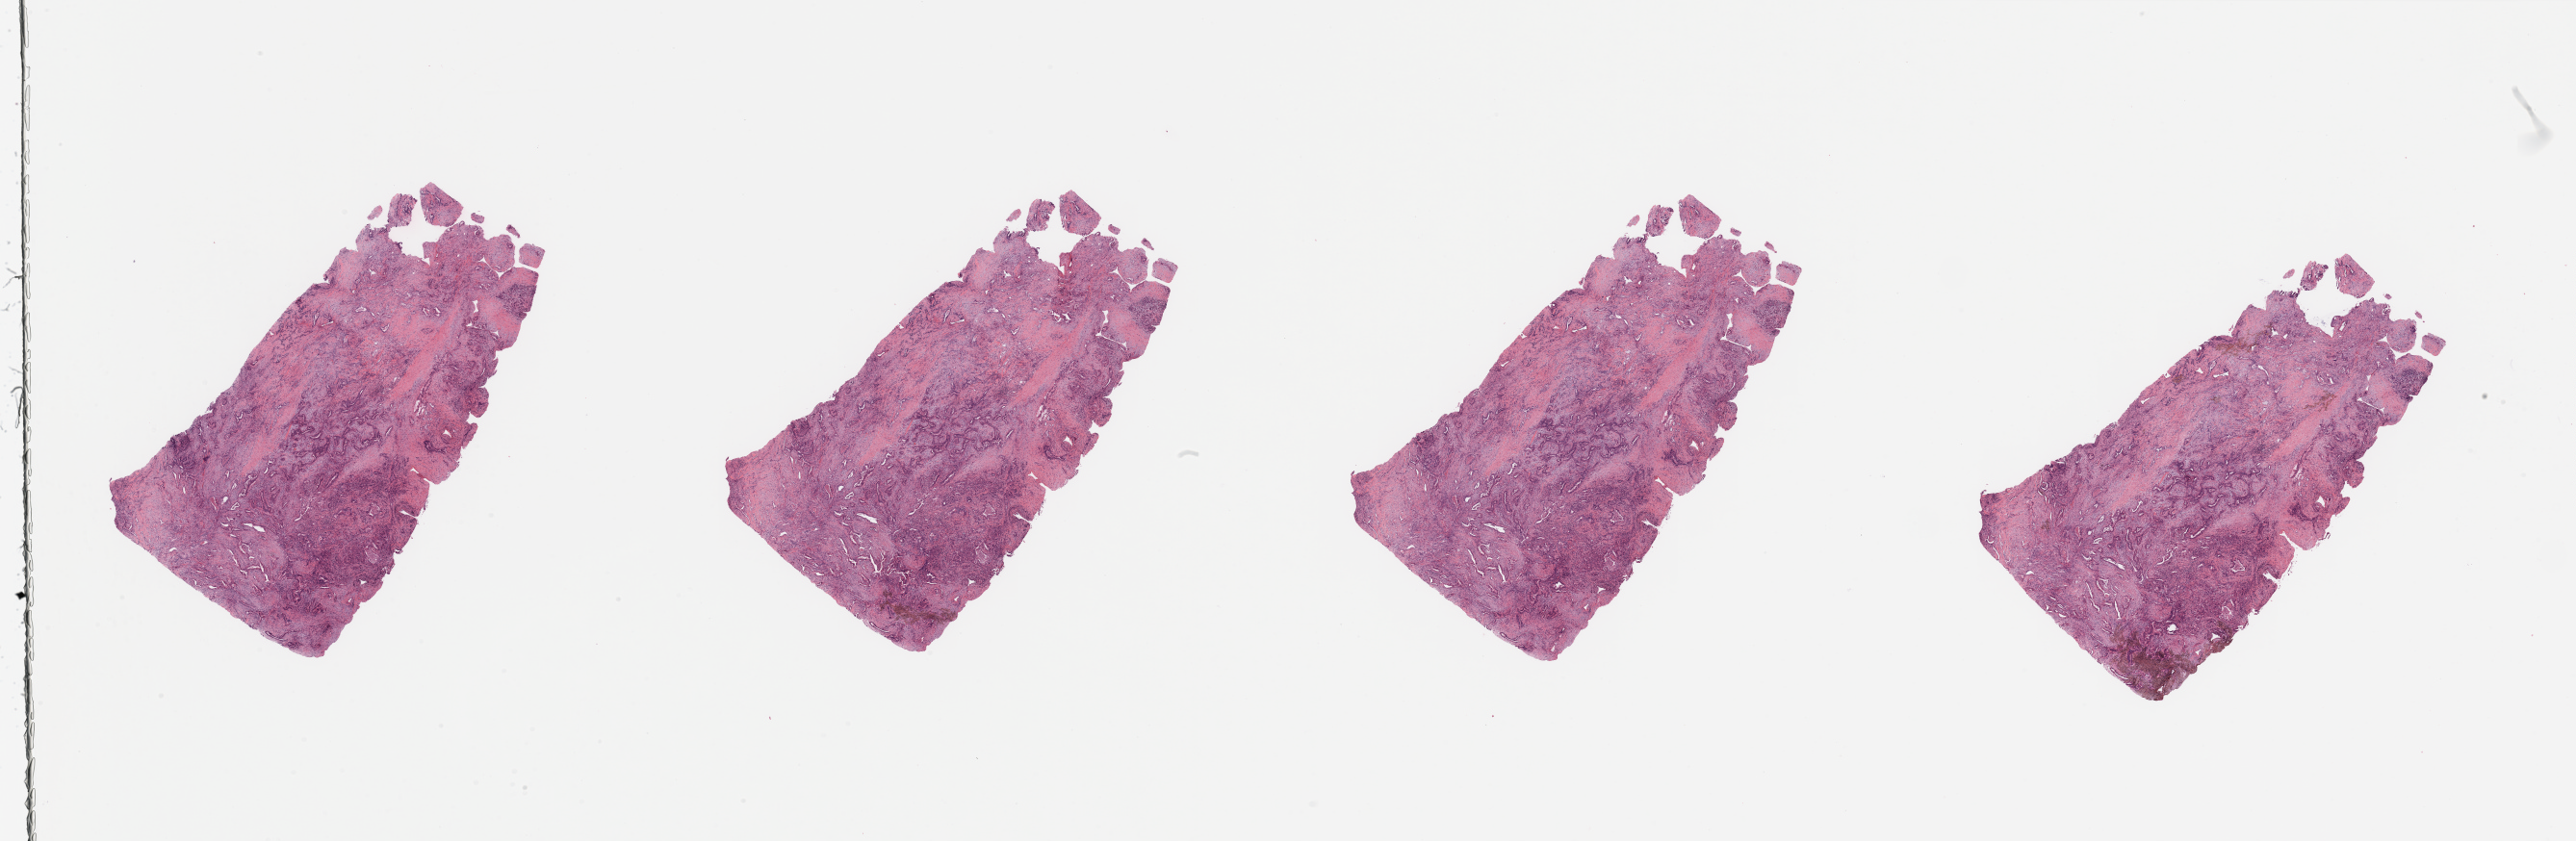
H&E-stained whole-slide image, whole scanned area (about 42.3 x 13.8 mm, slide scanned at 20x) shown as a low-resolution overview, tumour tissue sample, sampled site: pancreas. Male, 62 y/o. Histologic grade: G2 (moderately differentiated). Slide review estimates, as recorded: tumour nuclei 60%, necrosis 0%.
• AJCC pathologic stage: IIB
• primary tumour site (as recorded): head
• histologic diagnosis: Infiltrating duct carcinoma, NOS